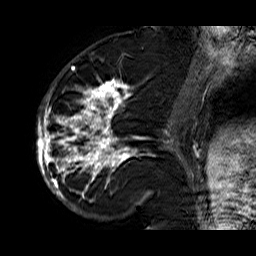
Breast MRI (dynamic contrast-enhanced), one sagittal slice; slice 24 of 60 in the series (ordered by position); dynamic contrast-enhanced series, time point 2 of 6 at this slice position (early post-contrast); 1.5 T; TE 6.3 ms, TR 32.9 ms; 256 × 256 image matrix. Female patient. Case-level facts recorded for this patient, not image findings: setting: breast cancer imaged before/during neoadjuvant chemotherapy; receptor status: HR-positive, HER2-negative.
Annotated regions visible in this slice (semi-automatic segmentation, software-assisted and operator-edited):
- analysis volume of interest (the breast-tissue region the enhancement analysis was run in; not a lesion): bounding box [x1, y1, x2, y2] px = [36, 74, 176, 210]
- tumour enhancement mask (voxels above the 100 % enhancement threshold inside the analysis volume of interest): [36, 77, 173, 209]